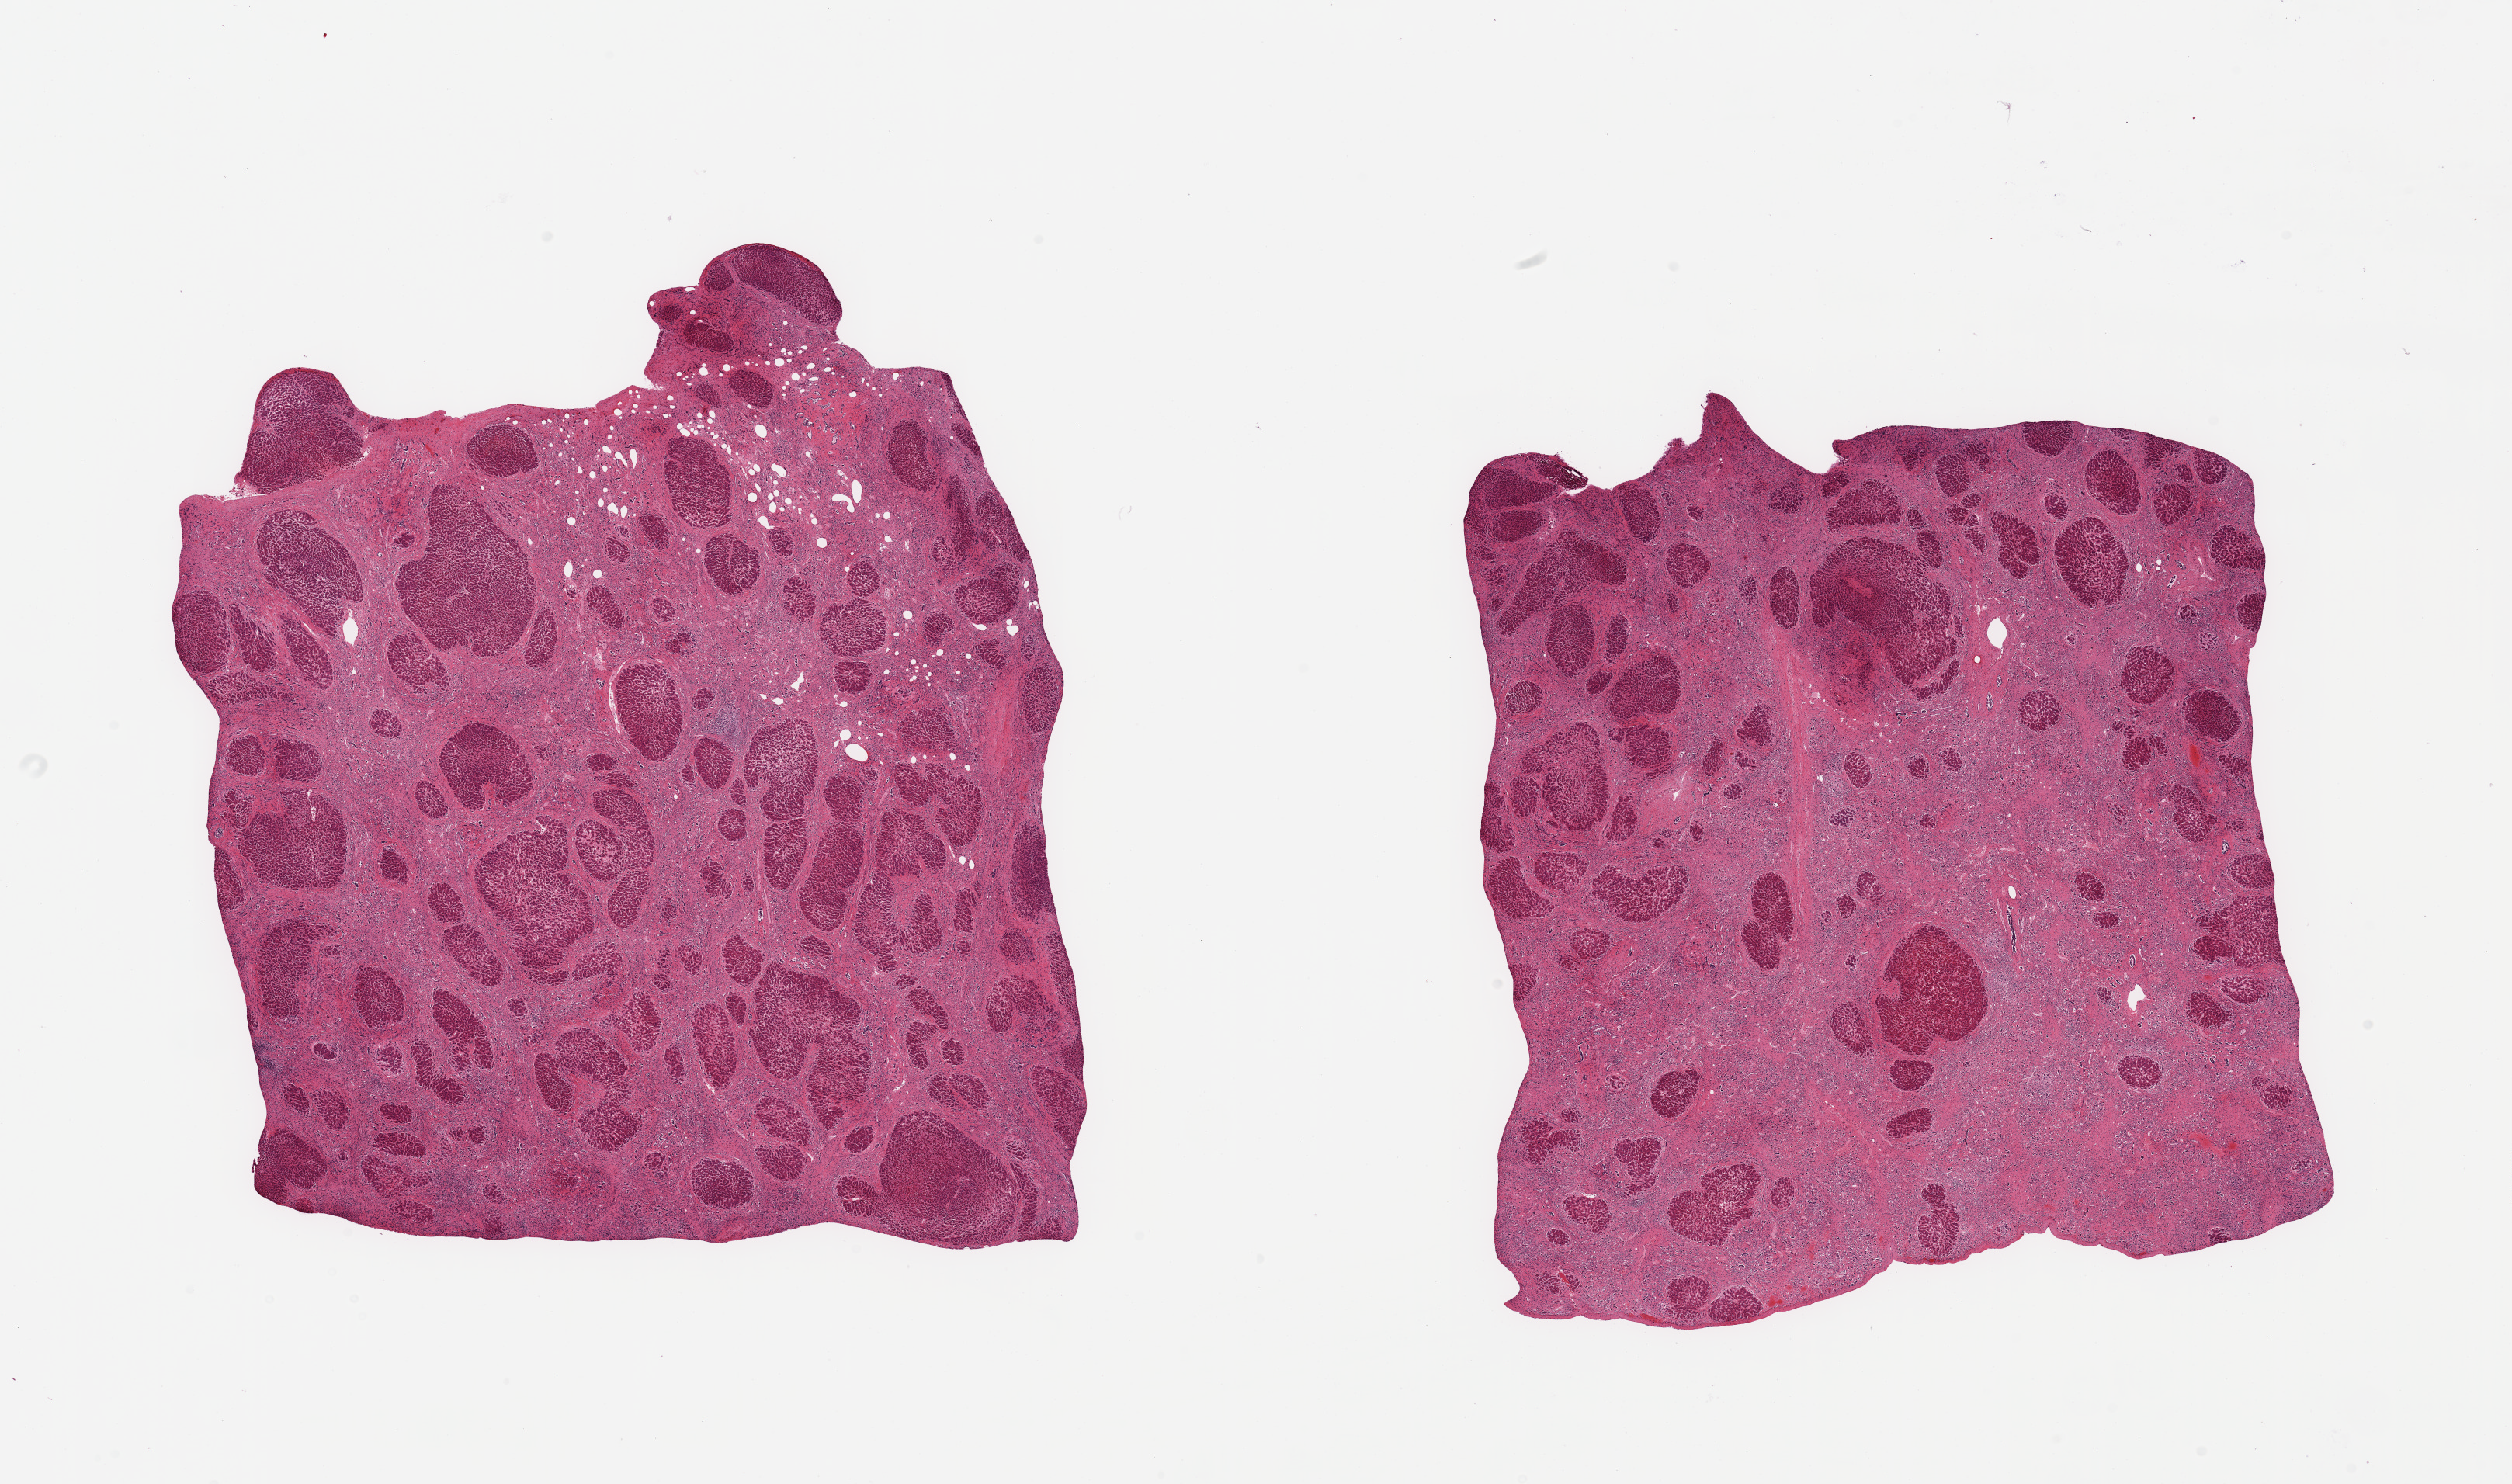
Digitized haematoxylin and eosin-stained section — shown as a low-resolution overview of the whole scanned area (about 25.6 x 15.1 mm, acquisition: 20x scan), PAXgene-fixed, paraffin-embedded tissue, section of liver (target tissue), donor tissue sample. Donor sex: male.
Reviewer comment on this tissue sample: 2 pieces; extensive cirrhosis with >50% fibrous content.